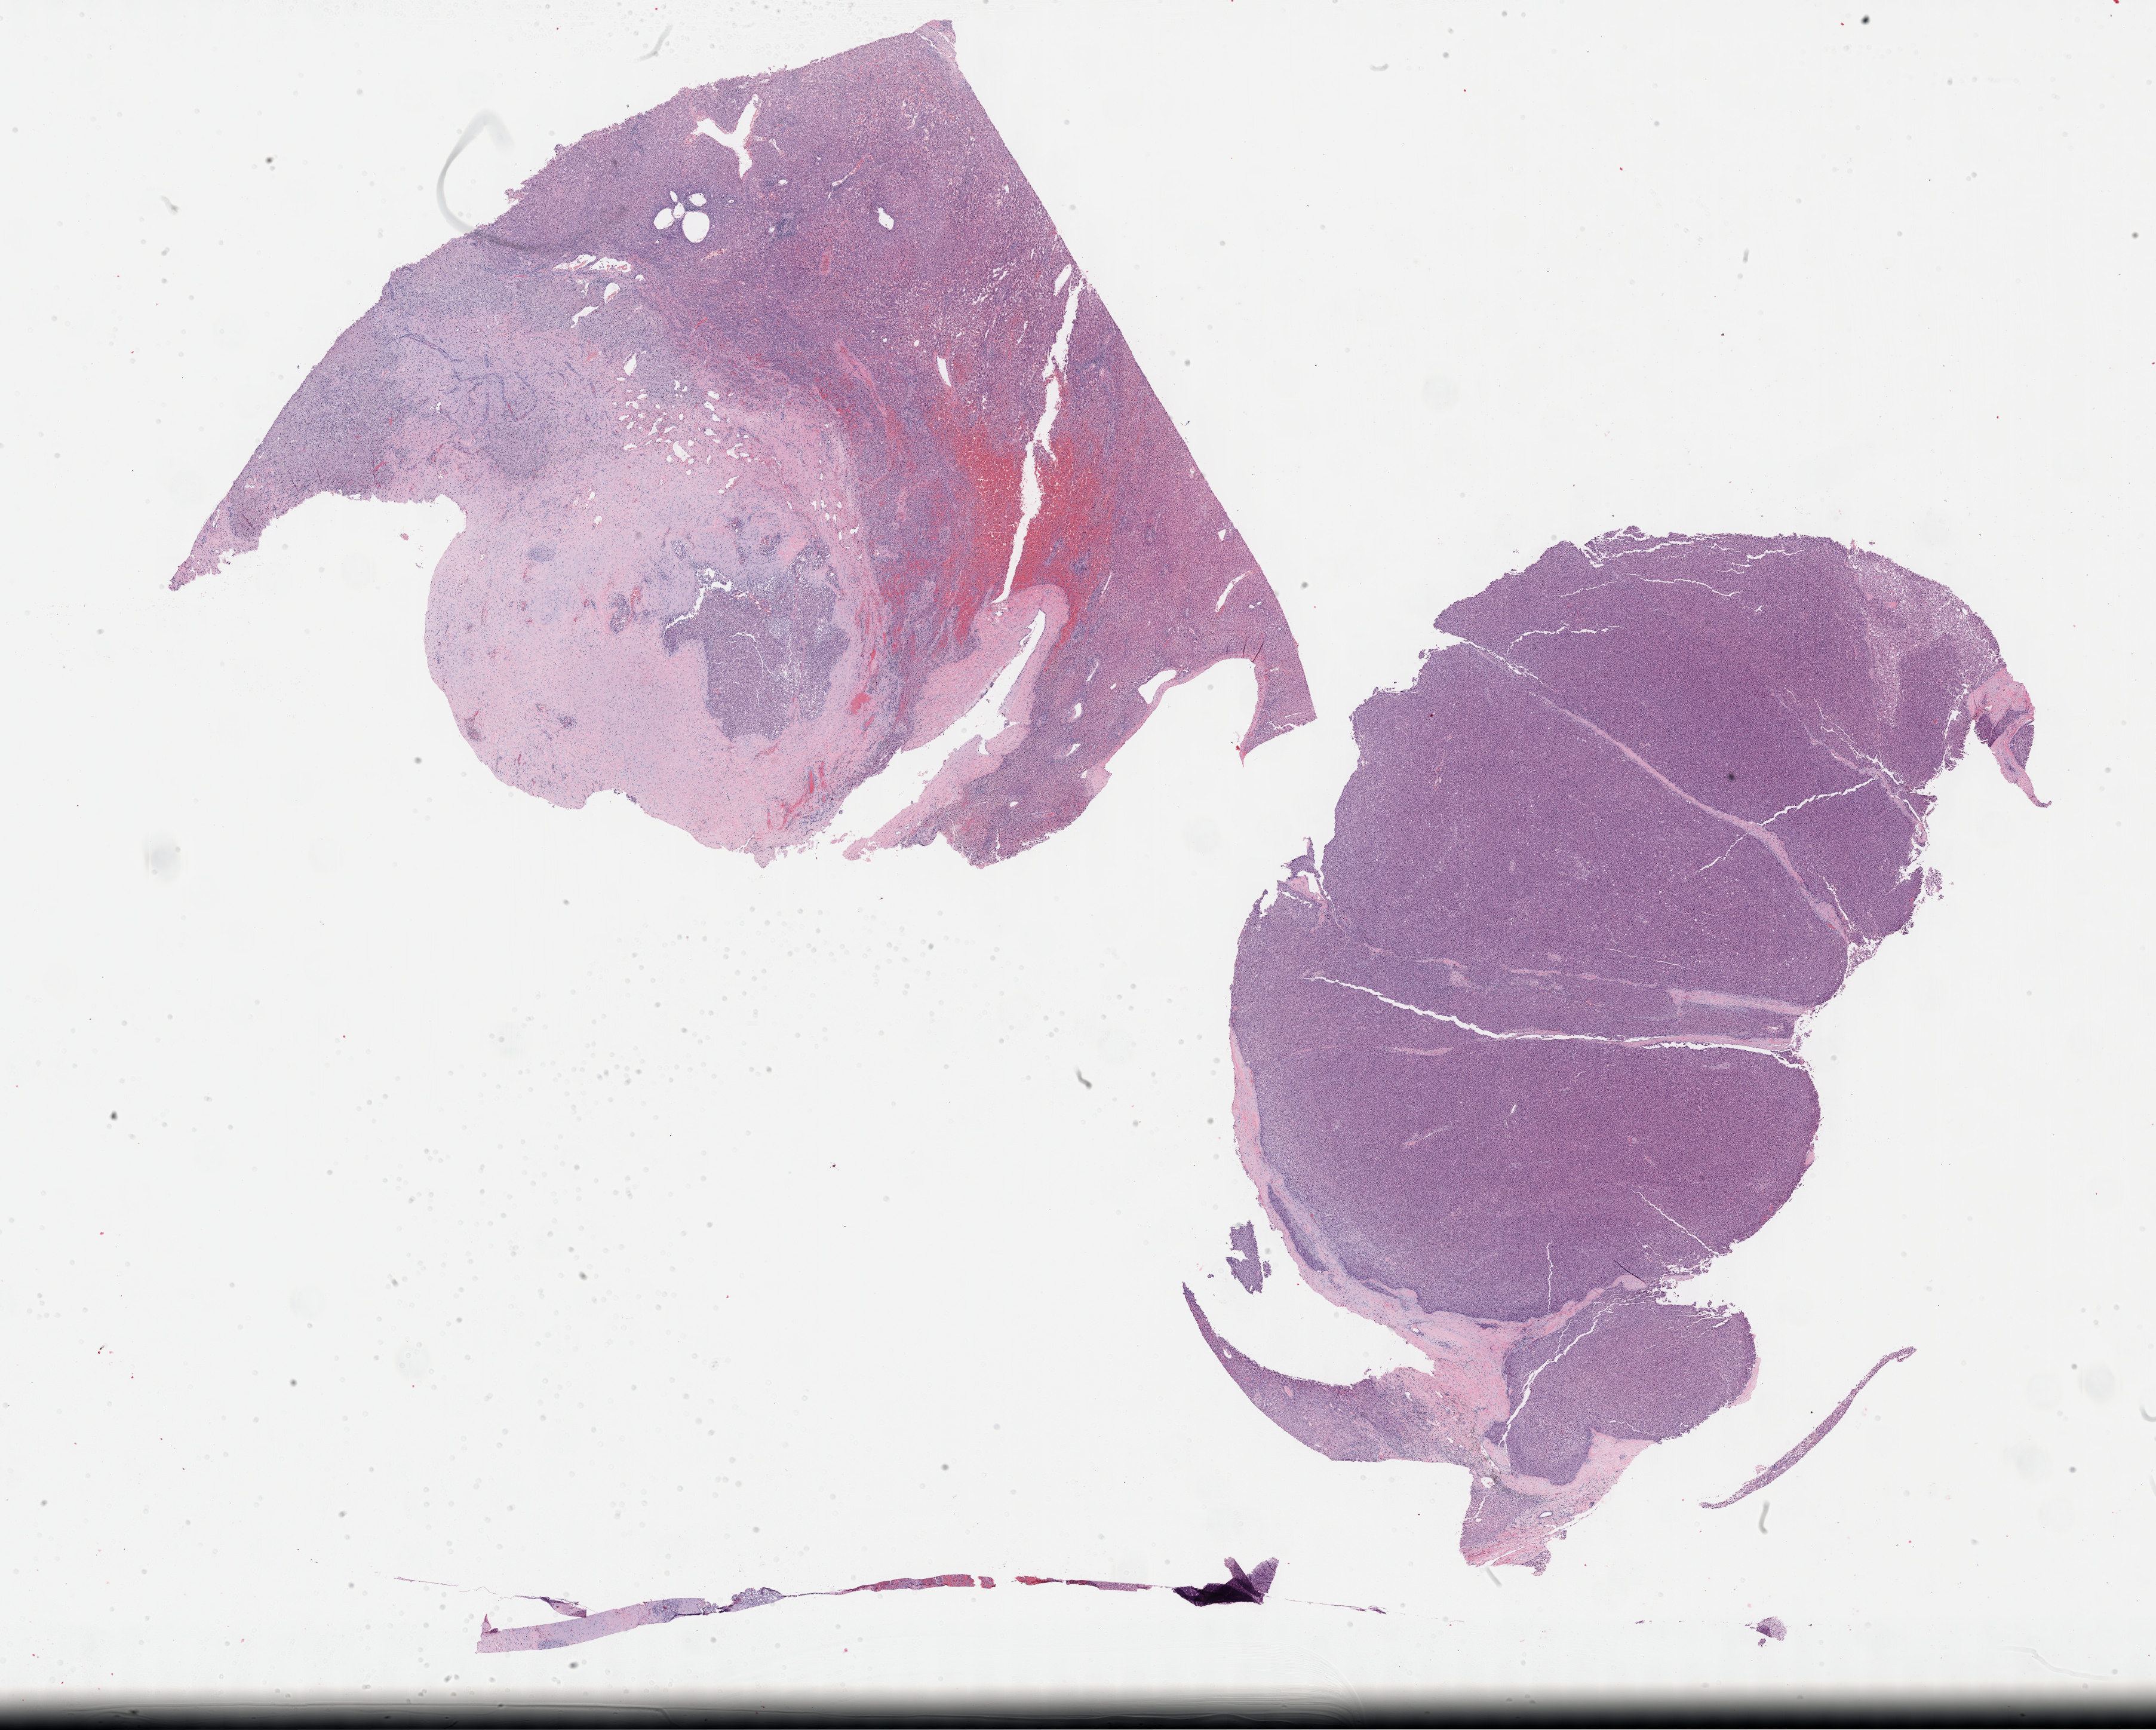
H&E-stained whole-slide image — whole scanned area (about 29.2 x 23.4 mm, acquisition: 40x scan) shown as a low-resolution overview; FFPE section; primary tumour sample from the liver. Male patient; age at initial diagnosis 48 years.
Diagnosis: Hepatocellular carcinoma, NOS.